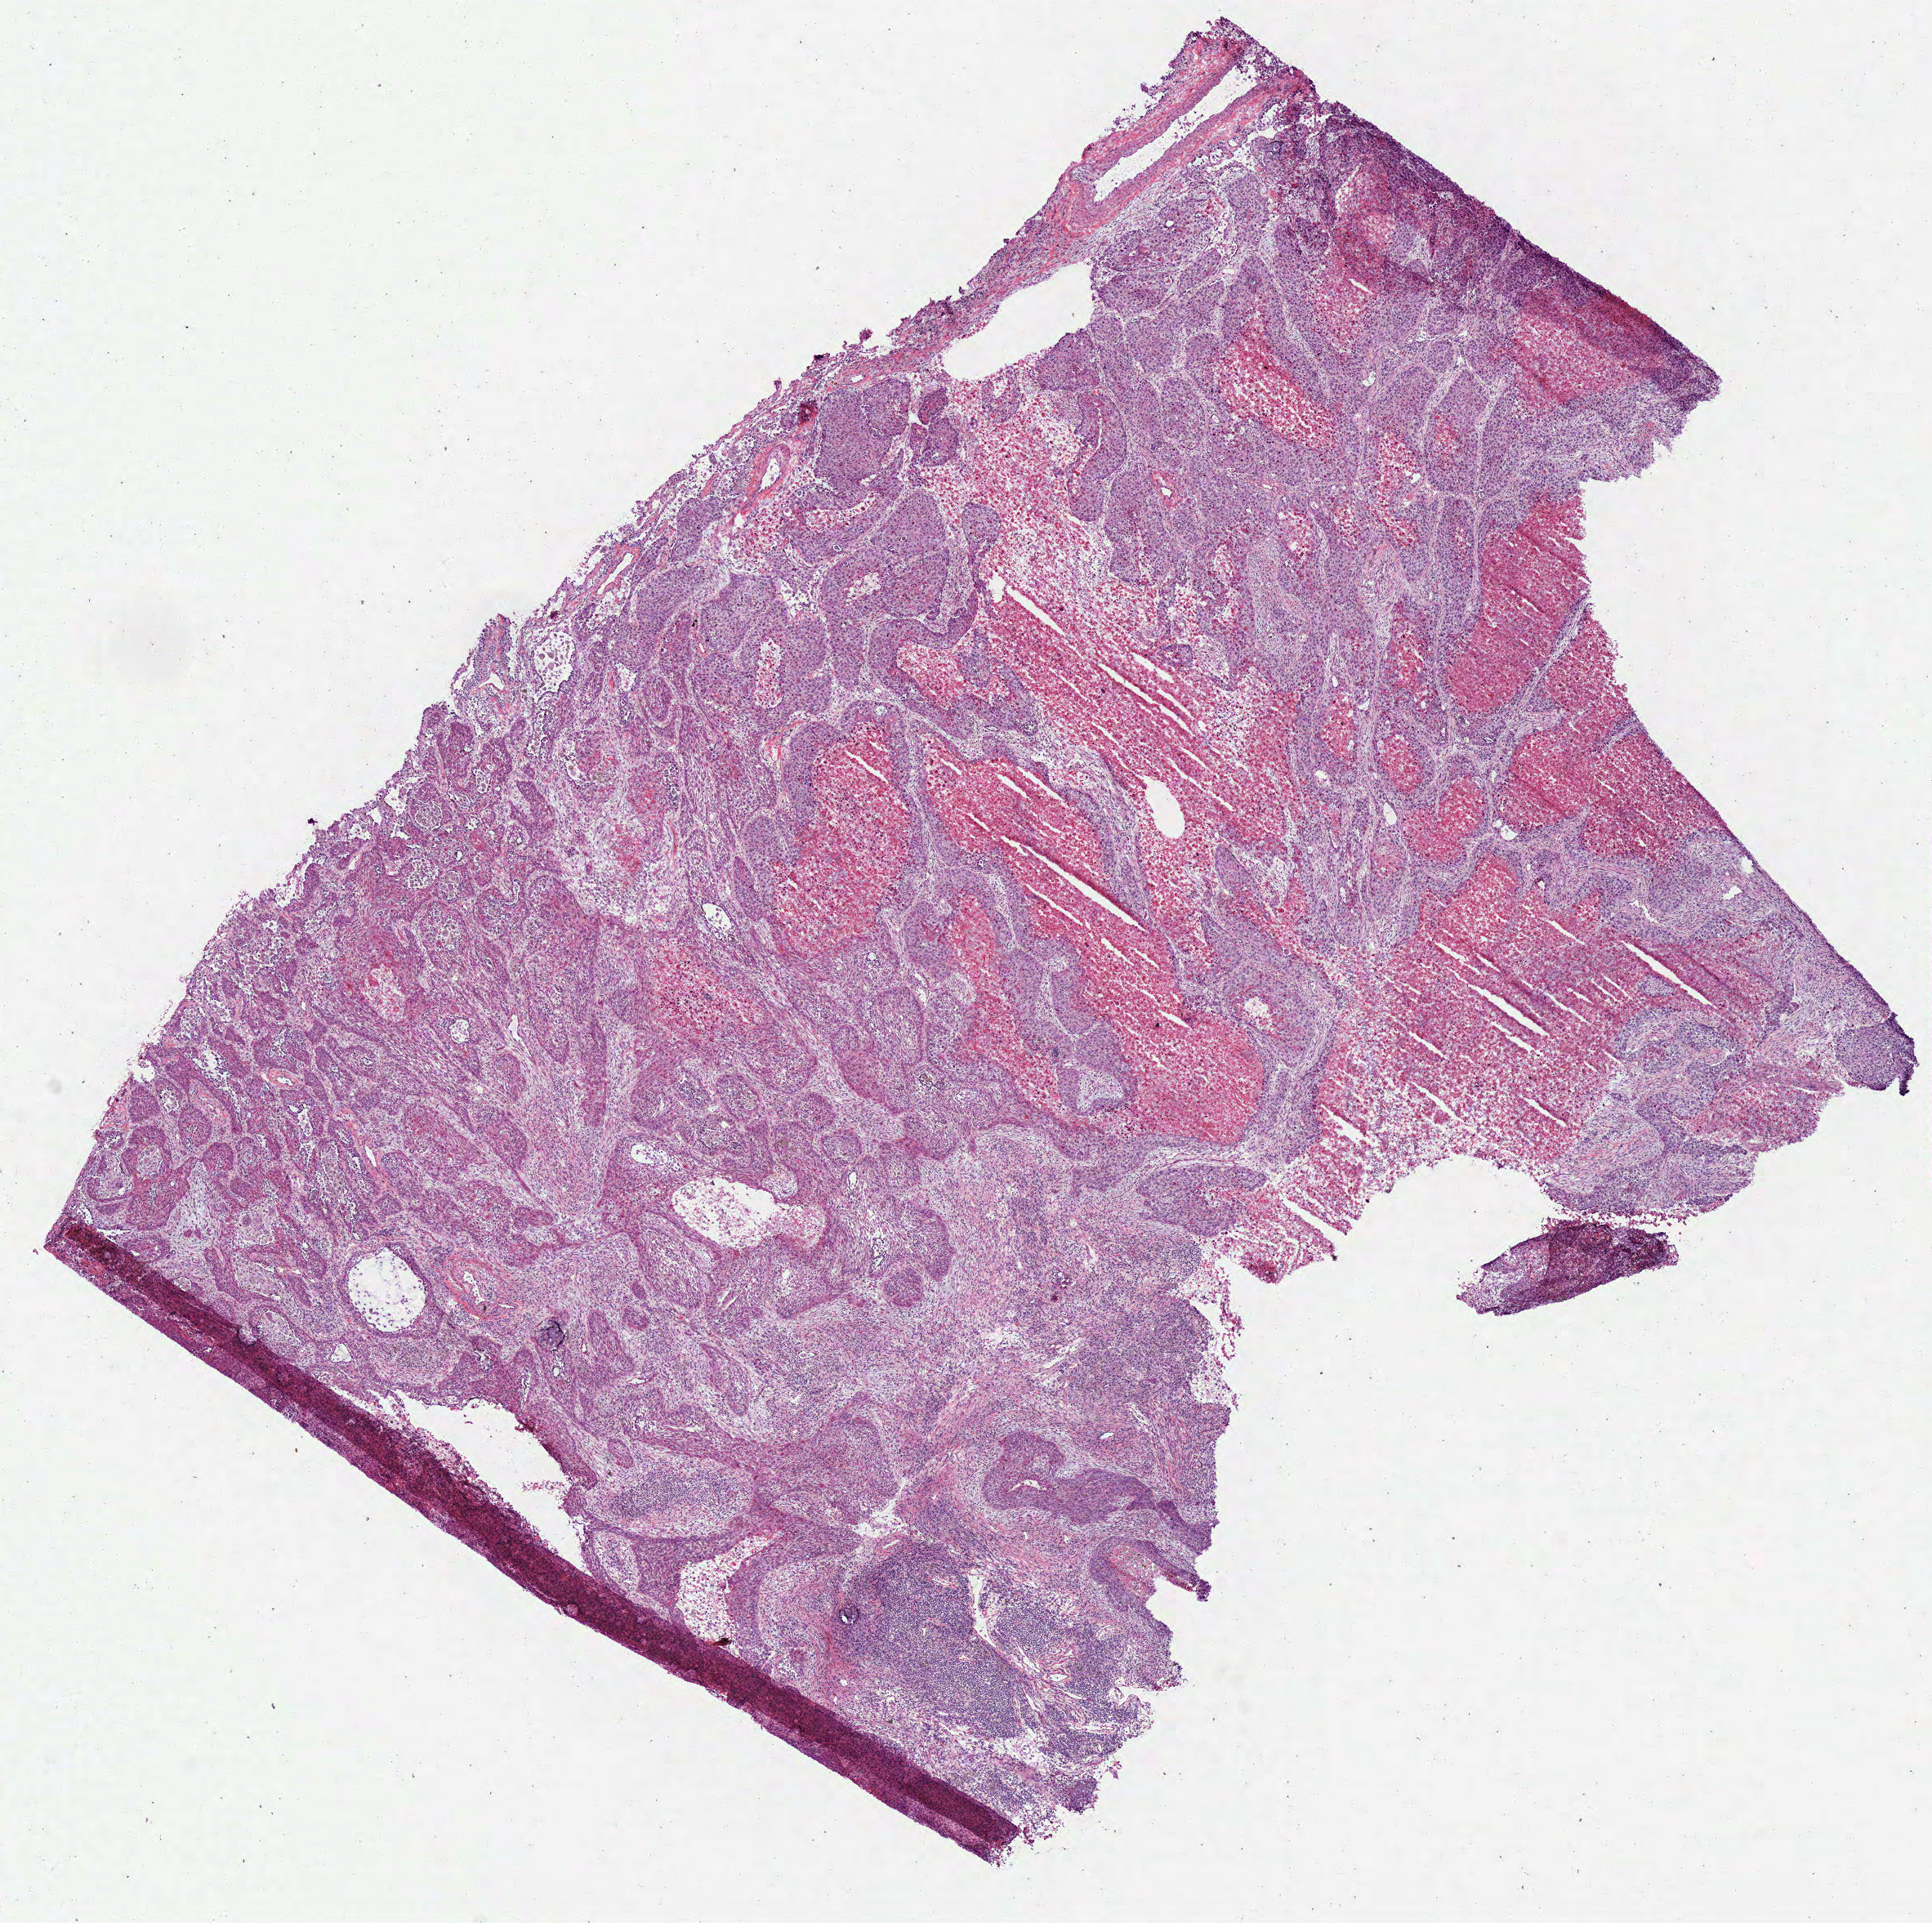
Whole-slide histology image, H&E — a low-resolution overview of the entire scanned area, about 9.3 x 9.3 mm (from a 40x scan). Frozen section from the bottom of the tissue portion. Lung, primary tumour sample. Patient: female, age at initial diagnosis 59 years. Composition of this section per pathologist review: tumour cells 69%, tumour nuclei 77%, normal cells 0%, stromal cells 0%, necrosis 31%. Inflammatory infiltration, as recorded: lymphocyte infiltration 20%, monocyte infiltration 0%, neutrophil infiltration 0%.
• AJCC pathologic stage: IB (7th edition)
• laterality: left
• pathologic diagnosis: Squamous cell carcinoma, NOS (upper lobe, lung)